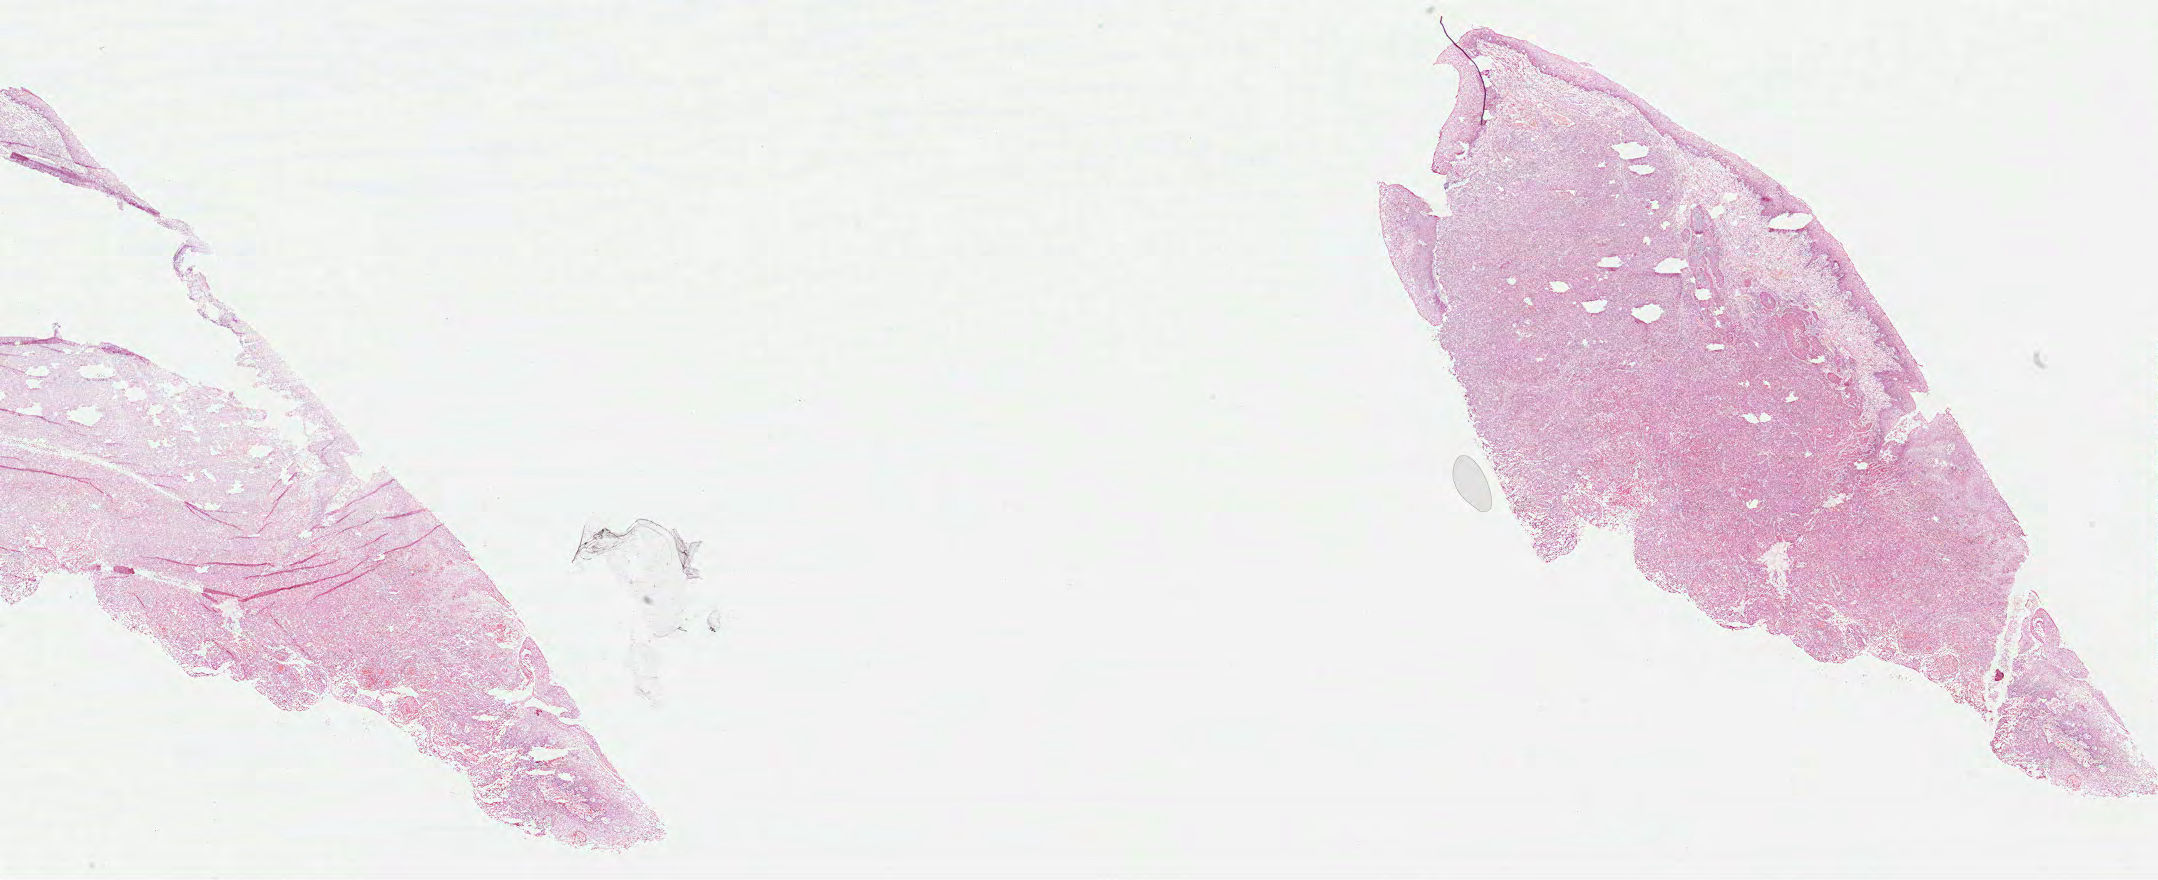
H&E whole-slide image, whole scanned area (about 34.8 x 14.2 mm, acquisition: 40x scan) shown as a low-resolution overview, formalin-fixed paraffin-embedded (FFPE) diagnostic section, sample: primary tumour, head and neck. Male, age 66 years at initial diagnosis. Histologic grade: G2 (moderately differentiated).
Pathologic diagnosis: Squamous cell carcinoma, NOS (hypopharynx, NOS). AJCC pathologic stage: IVA. TNM: T4a N2b.